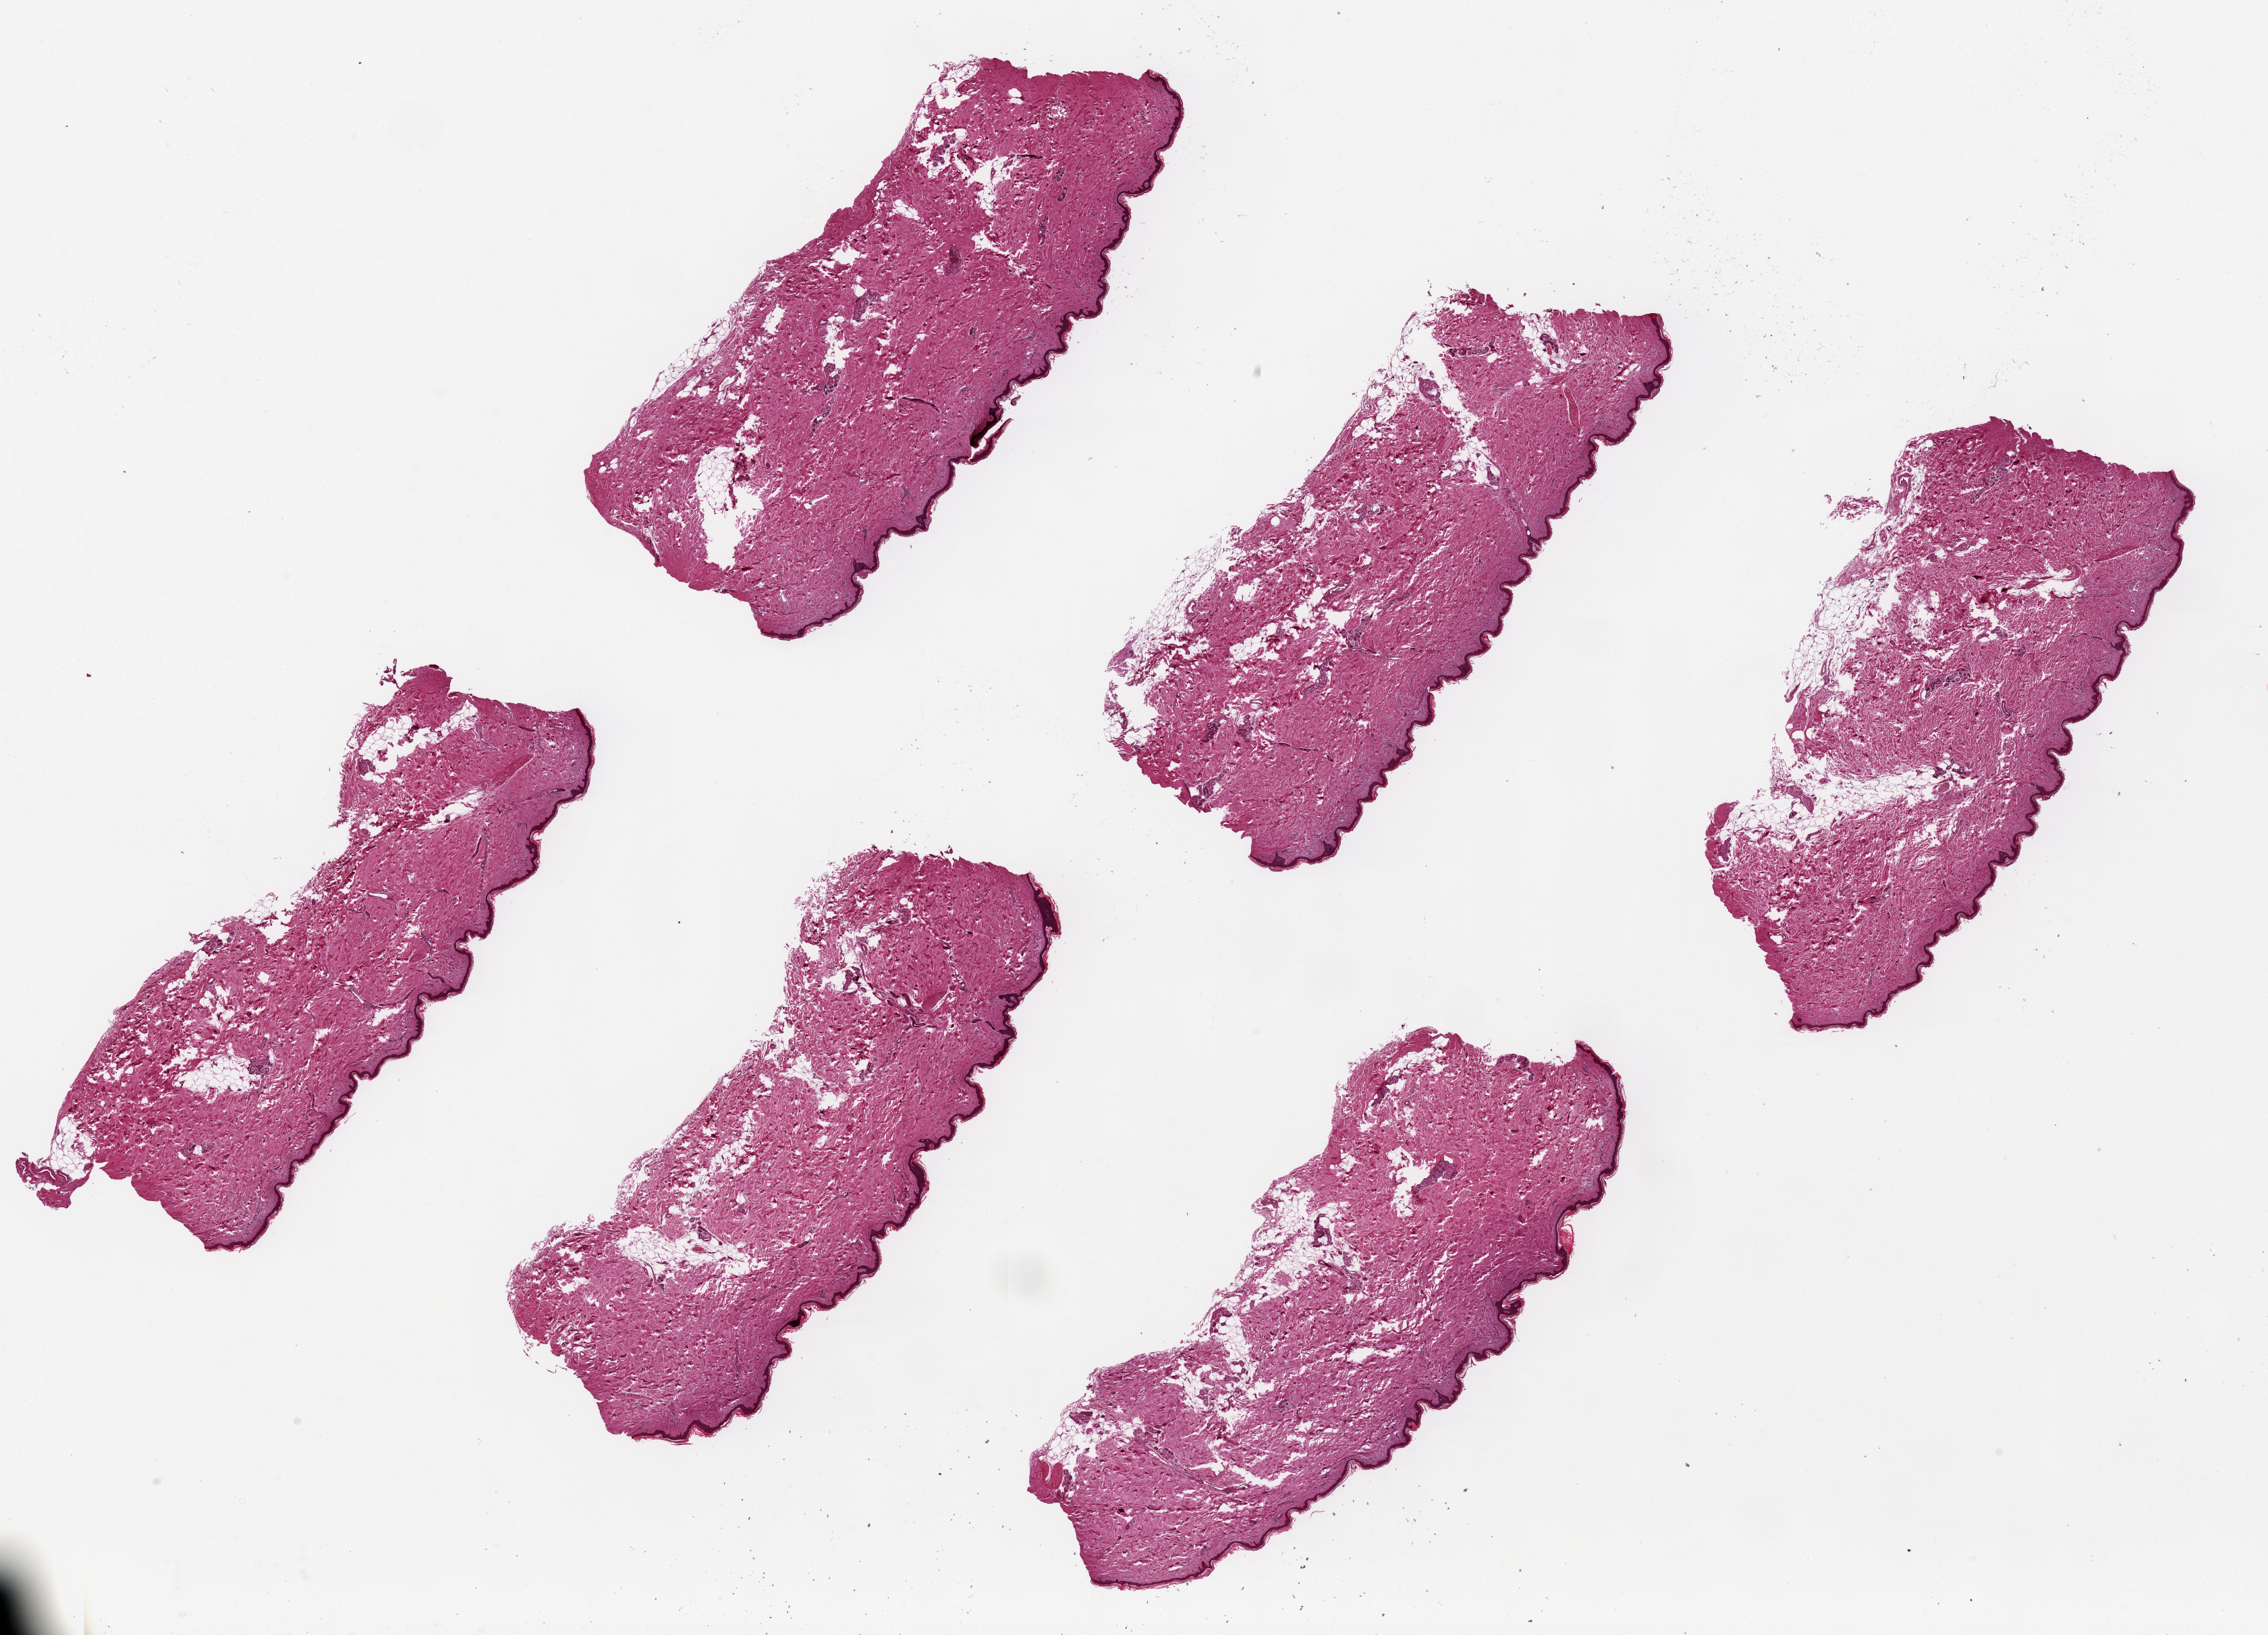
Digitized H&E-stained section, brightfield — a low-resolution overview of the entire scanned area, about 26.6 x 19.2 mm (slide scanned at 20x); PAXgene-fixed, paraffin-embedded tissue; sampled site (target tissue): skin of lower leg; tissue donor sample. Donor: female.
- review note (as recorded): 6 pieces, ~7.5x3mm; squamous epithelium is ~1-2% of thickness